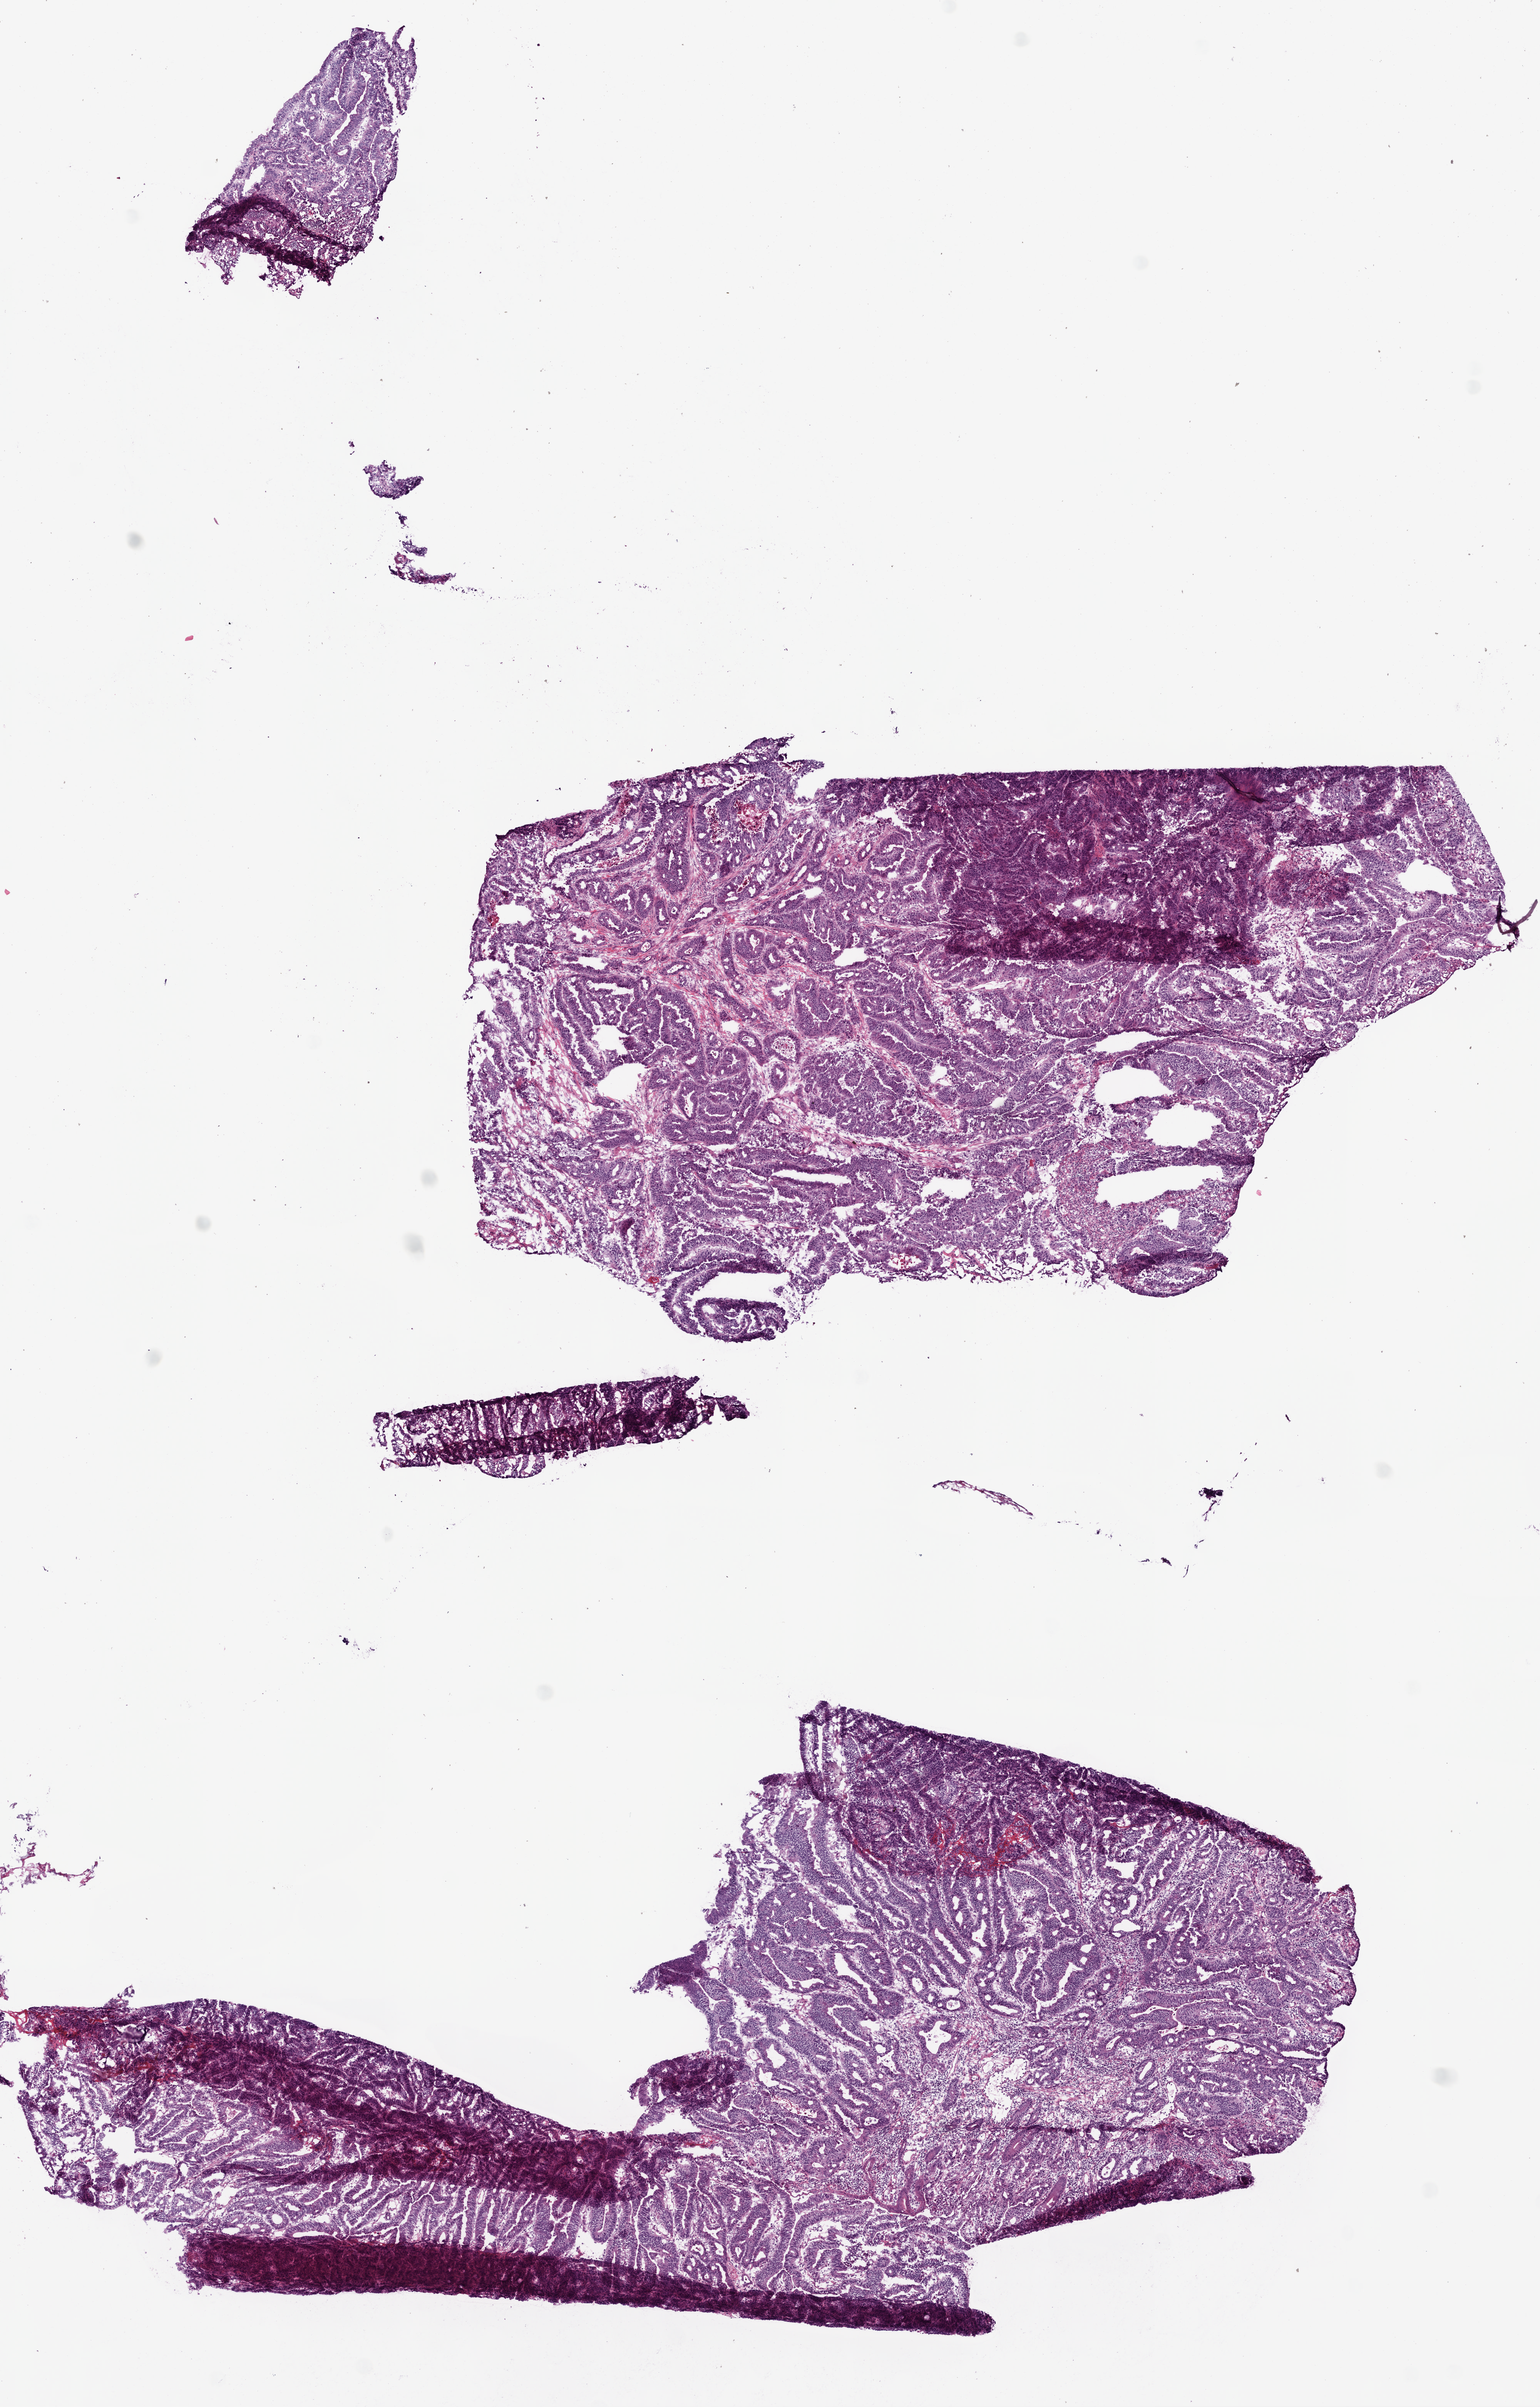
Whole-slide histology image, Hematoxylin and eosin (H&E) stained — low-resolution overview of the scanned area, about 8.0 x 12.5 mm. Frozen section from the bottom of the tissue portion. Sample: primary tumour, colon. Male, age 68 years at initial diagnosis. Slide review estimates, as recorded: tumour cells 100%, tumour nuclei 80%, normal cells 0%, stromal cells 0%, necrosis 0%.
Lymph nodes positive (case pathology): 2 of 41 examined. TNM: T3 N1 M0. AJCC pathologic stage: III (5th edition). Pathologic diagnosis: Adenocarcinoma, NOS.